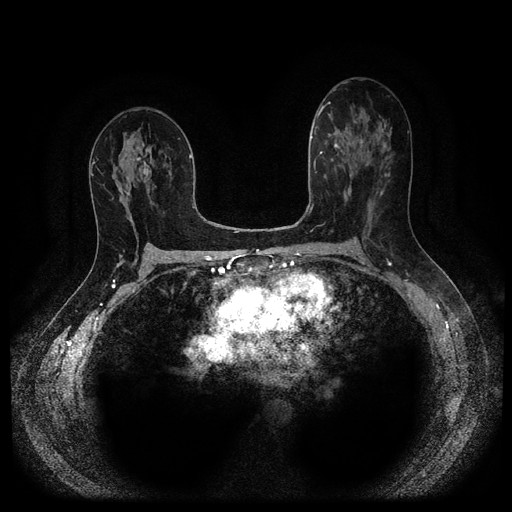
Breast MRI (dynamic contrast-enhanced, multi-phase), one axial slice; slice 55 of 116 in the series (ordered by position); dynamic contrast-enhanced series, time point 2 of 5 at this slice position (early post-contrast); 1.5 T; TE 2.6 ms, TR 5.3 ms; 512 × 512 image matrix, field of view 340 × 340 mm. Patient: female, 50 years.
Structures marked on this image (semi-automatic segmentation, software-assisted and operator-edited):
- breast lesion (labelled 'tumour' in the annotation; benign lesions carry a separate 'benign' label): box from (x=133, y=150) to (x=151, y=175) px